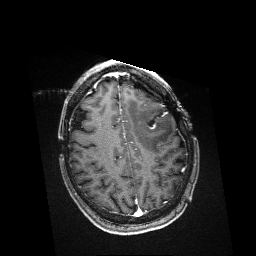
Brain MRI from a brain-tumour surgery series, one axial slice. Position 122 of 176 along the scan axis. T1-weighted post-contrast. 1 mm slice thickness. 256 × 256 image matrix, field of view 256 × 256 mm. Case-level facts recorded for this patient, not image findings: histopathology: Metastatic Melanoma; tumour location: Left Frontal.
Structures marked on this image (expert manual segmentation):
- residual tumour: bounding box <149,124,156,129> (left, top, right, bottom; pixels)